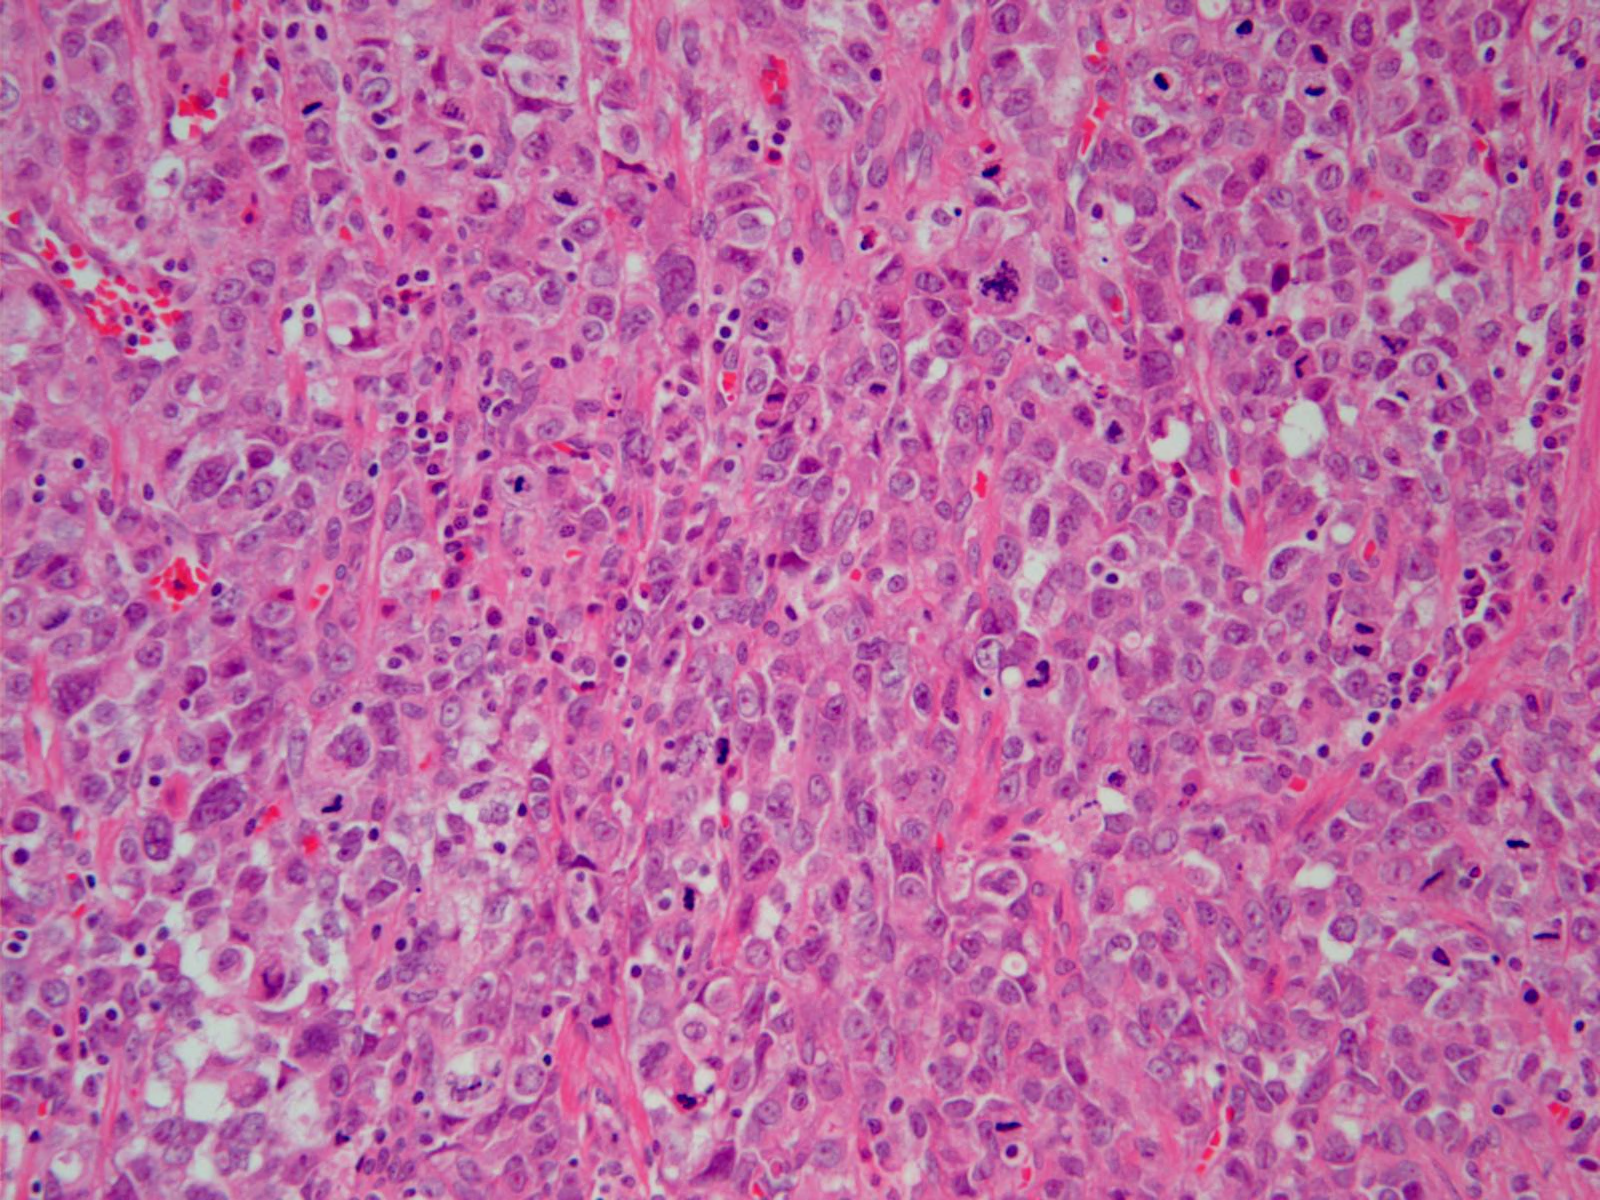
Single-field Hematoxylin and eosin (H&E) stained photomicrograph, roughly 0.8 x 0.6 mm in extent, formalin-fixed paraffin-embedded (FFPE) diagnostic section, primary tumour sample from the stomach. Patient: female, age at initial diagnosis 76 years. Histologic grade: G3 (poorly differentiated).
AJCC pathologic stage: IIIA (6th edition). Lymph nodes positive (case pathology): 4 of 12 examined. Diagnosis: Adenocarcinoma, NOS.